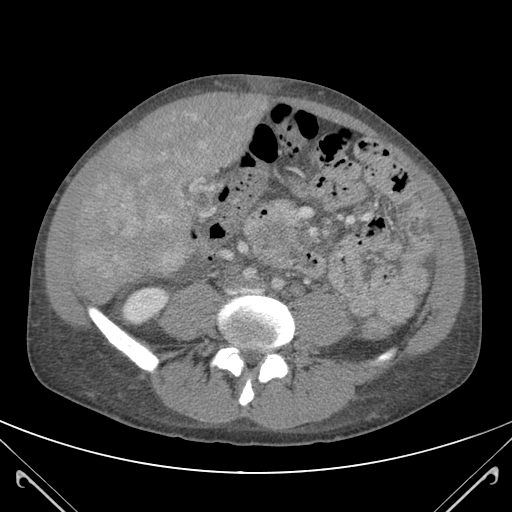
Contrast-enhanced abdominal CT (liver protocol), one axial slice. Slice 32 of 118 in the series (ordered by position). 120 kVp. Soft-tissue window (W 400 / L 40 HU). 3 mm slice thickness. 512 × 512 image matrix, field of view 380 × 380 mm. From the clinical record (not read from this slice): diagnosis: hepatocellular carcinoma (patient treated with transarterial chemoembolisation; whether this scan precedes or follows treatment is not stated here); TNM stage (as recorded): Stage-IIIB; Child-Pugh class: A; tumour nodularity: uninodular.
Structures marked on this image (semi-automatic segmentation, software-assisted and operator-edited):
- mass: bounding box <83,94,250,279> (left, top, right, bottom; pixels)